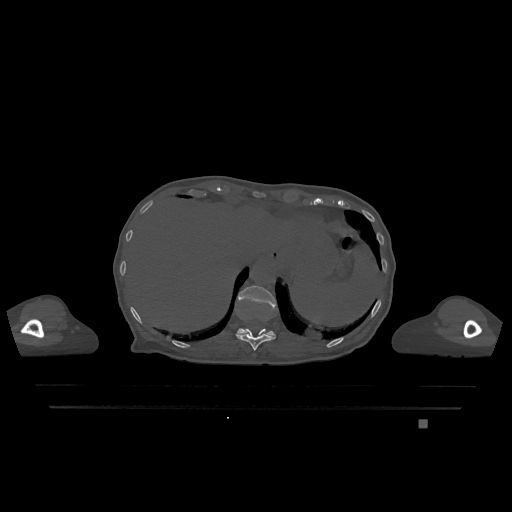
CT including the spine, one axial slice; slice 570 of 1317 in the series (ordered by position); bone window (W 1800 / L 400 HU); 0.5 mm slice thickness; 512 × 512 image matrix, field of view 500 × 500 mm. Patient: female, 74 years. From the clinical record (not read from this slice): primary cancer: lung.
Outlined on this slice (semi-automatic segmentation, software-assisted and operator-edited):
- T11 vertebra: bounding box (x1, y1, x2, y2) in pixels: (236, 329, 276, 351)
- T12 vertebra: (237, 285, 276, 337)